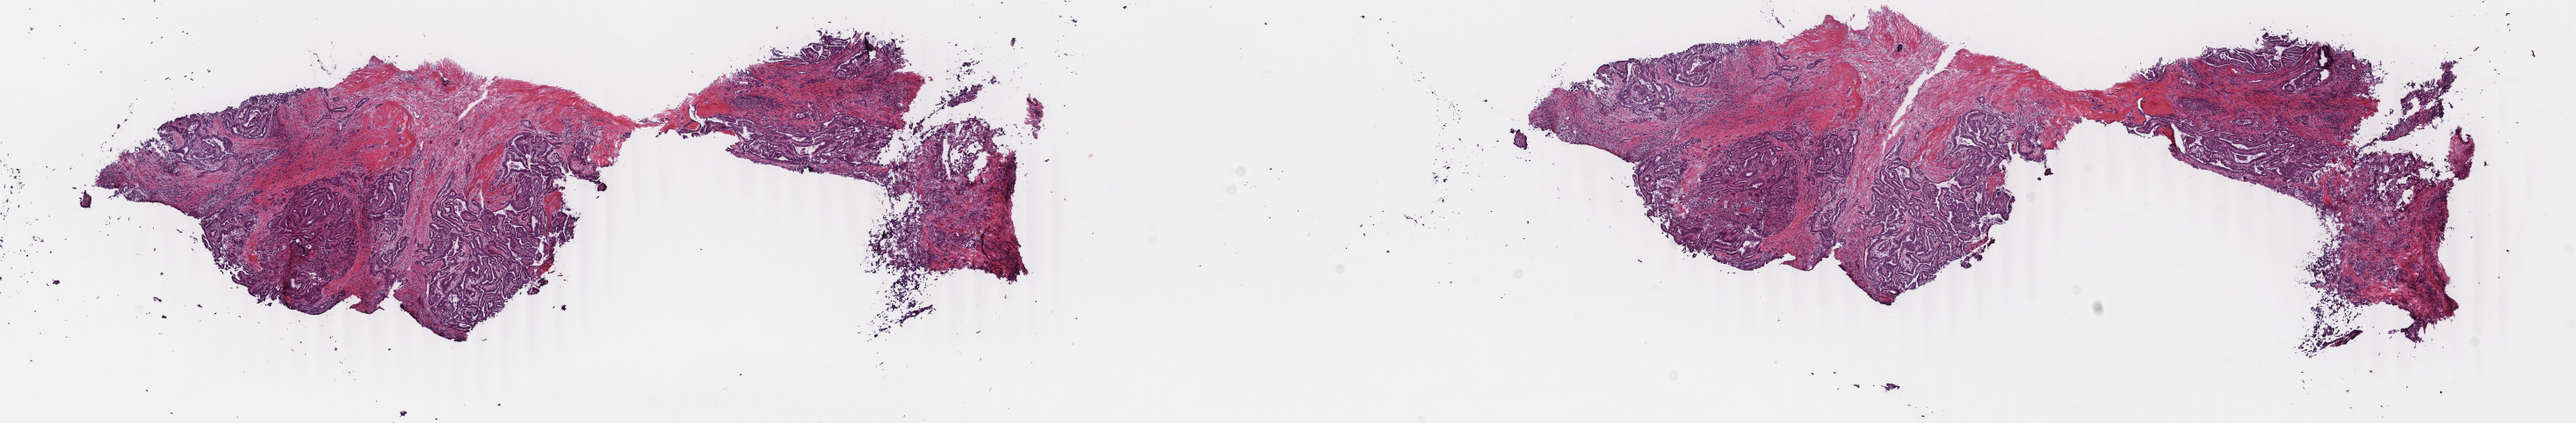
Digitized Hematoxylin and eosin (H&E) stained tissue section (whole slide), low-resolution overview of the scanned area, about 23.3 x 3.8 mm (from a 40x scan). Frozen section from the top of the tissue portion. Sample: primary tumour, thyroid. Male patient; age at initial diagnosis 85 years.
Diagnosis: Papillary carcinoma, columnar cell (thyroid gland).